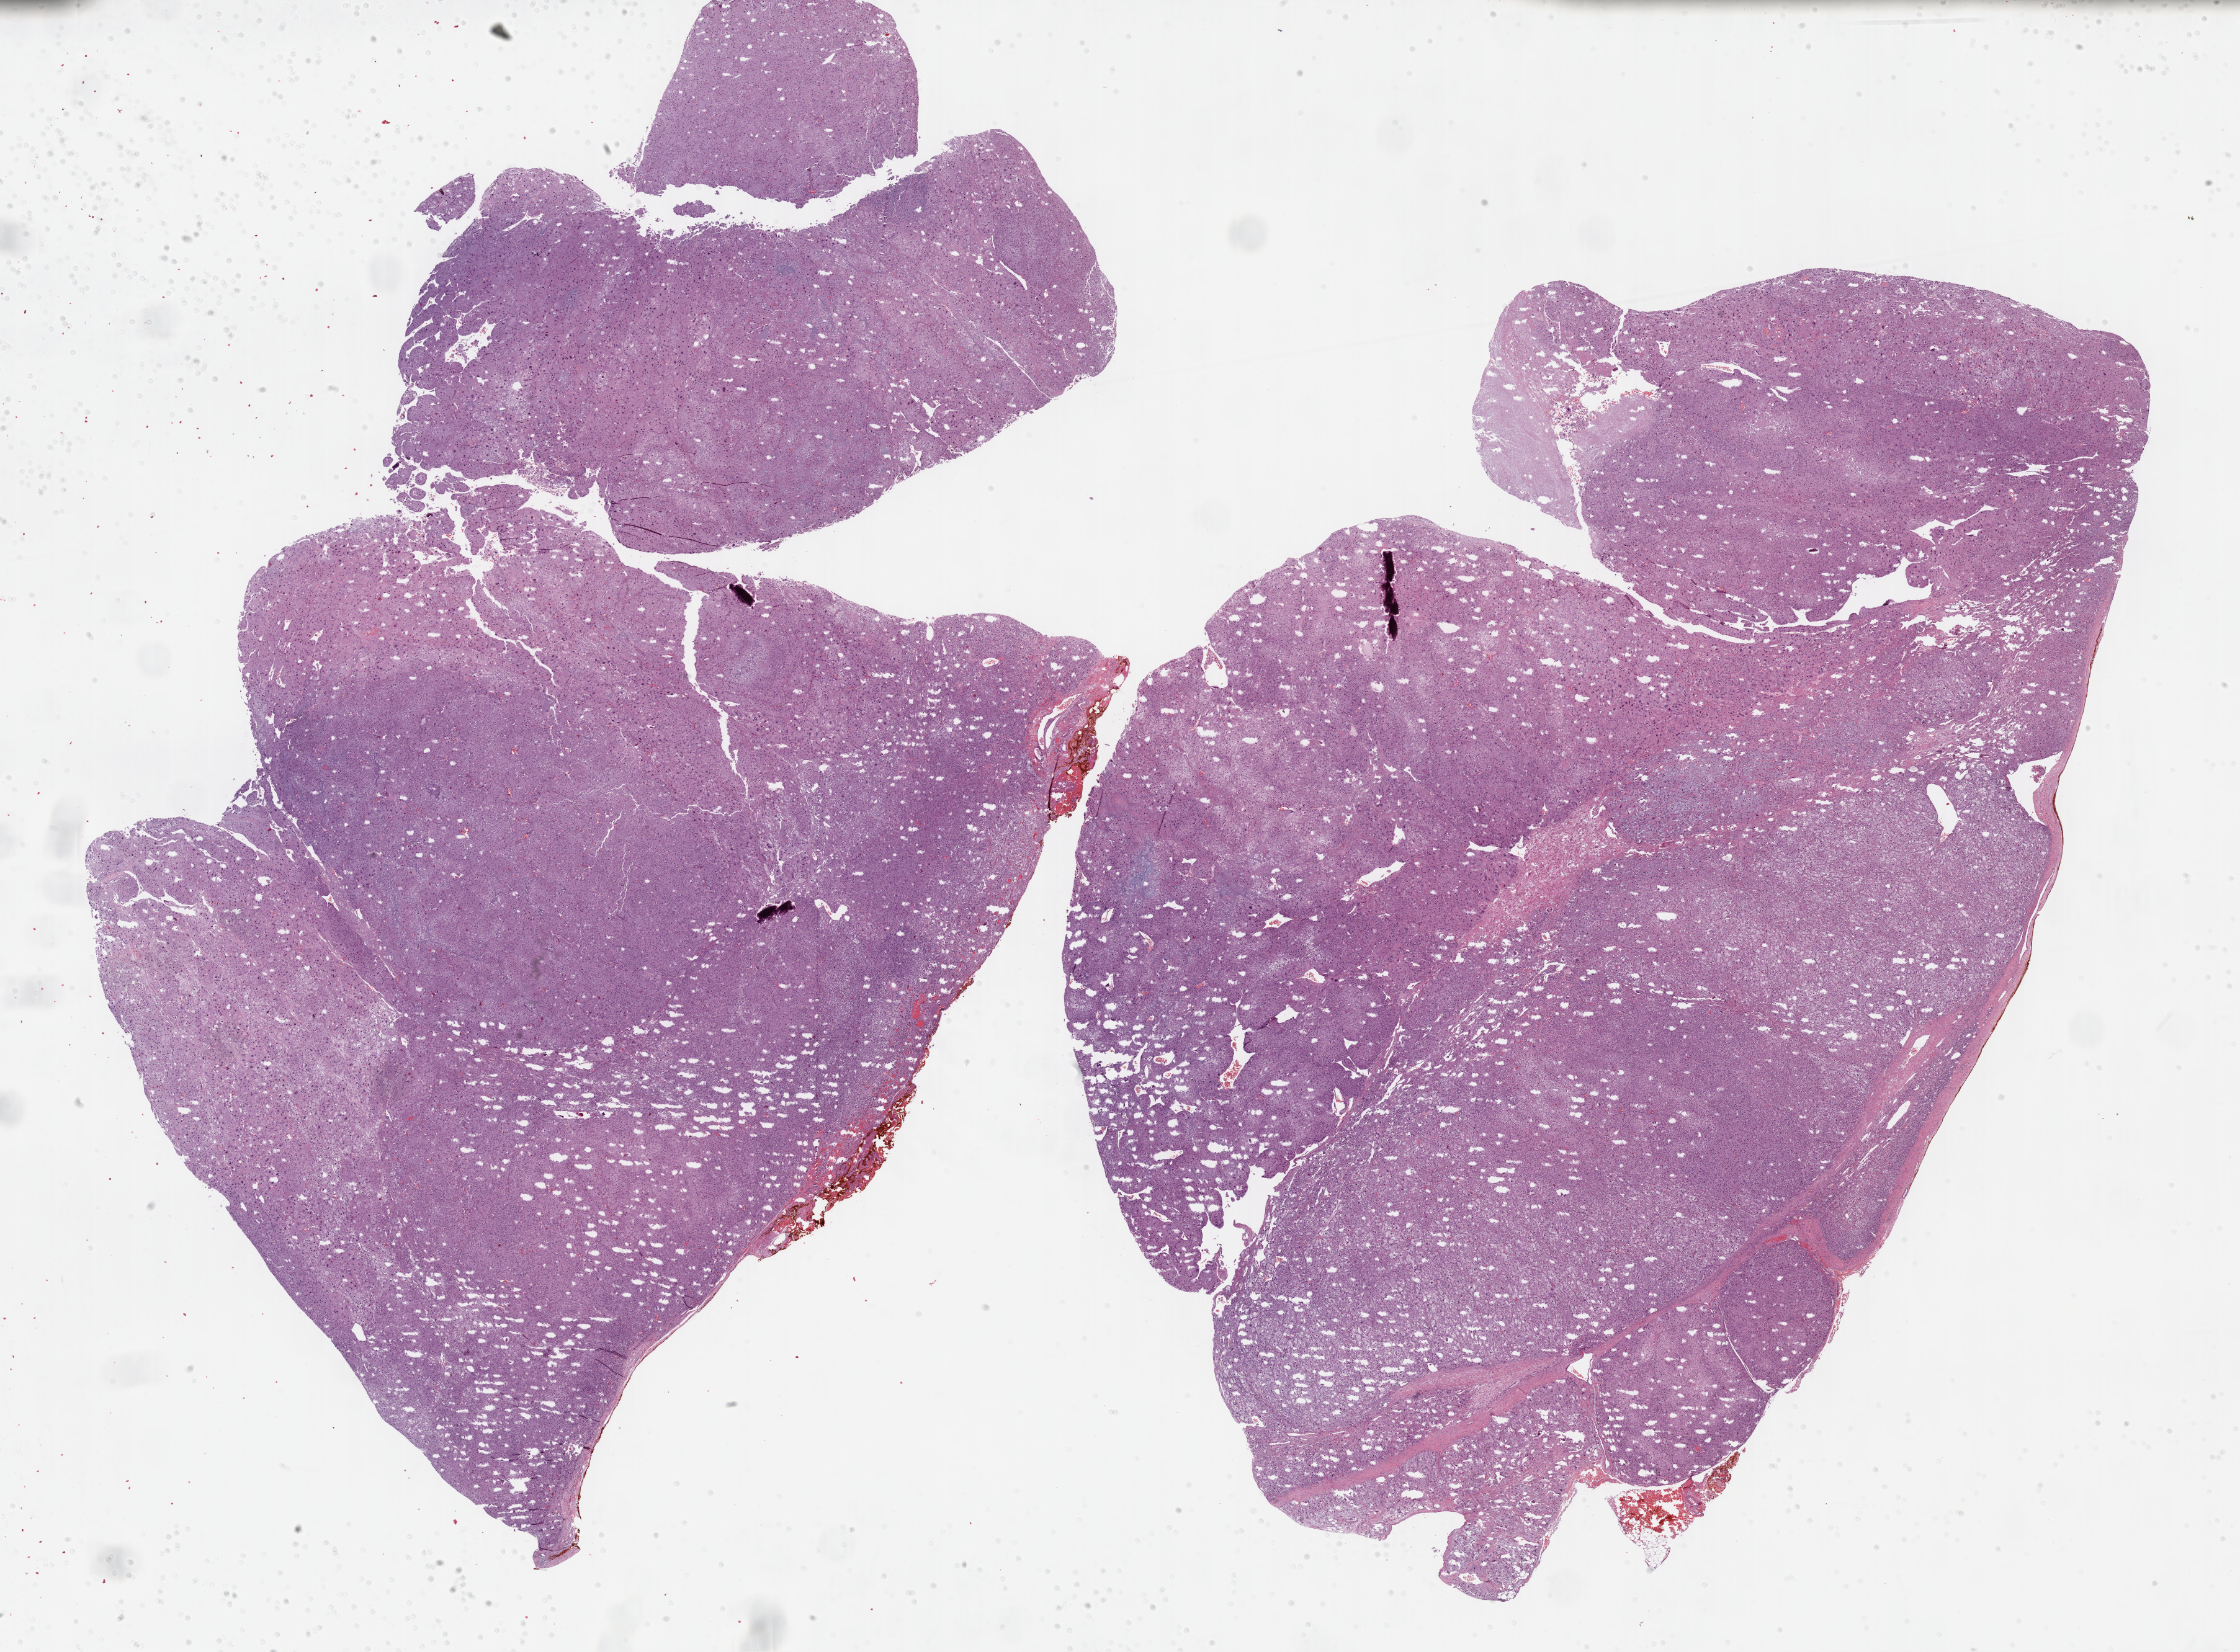
Whole-slide histology image, H&E-stained — a low-resolution overview of the entire scanned area, about 29.2 x 21.5 mm (from a 40x scan). FFPE section. Primary tumour sample from the adrenal cortex. Female, age 56 years at initial diagnosis.
Histologic diagnosis: Adrenal cortical carcinoma (cortex of adrenal gland).